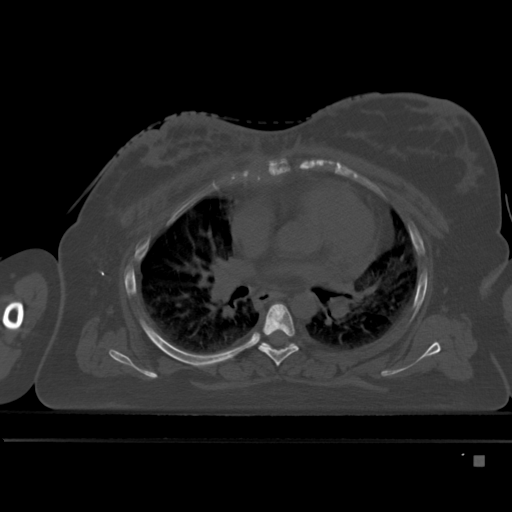
CT including the spine, one axial slice. Bone window (W 1800 / L 400 HU). 1.5 mm slice thickness. 512 × 512 image matrix, field of view 404 × 404 mm. Patient: female, 33 years. Case-level facts recorded for this patient, not image findings: primary cancer: breast; vertebrae with lytic lesions (as recorded): T1.
Structures marked on this image (semi-automatic segmentation, software-assisted and operator-edited):
- T5 vertebra: bounding box <259,303,299,366> (left, top, right, bottom; pixels)
- T6 vertebra: <259,342,297,348>